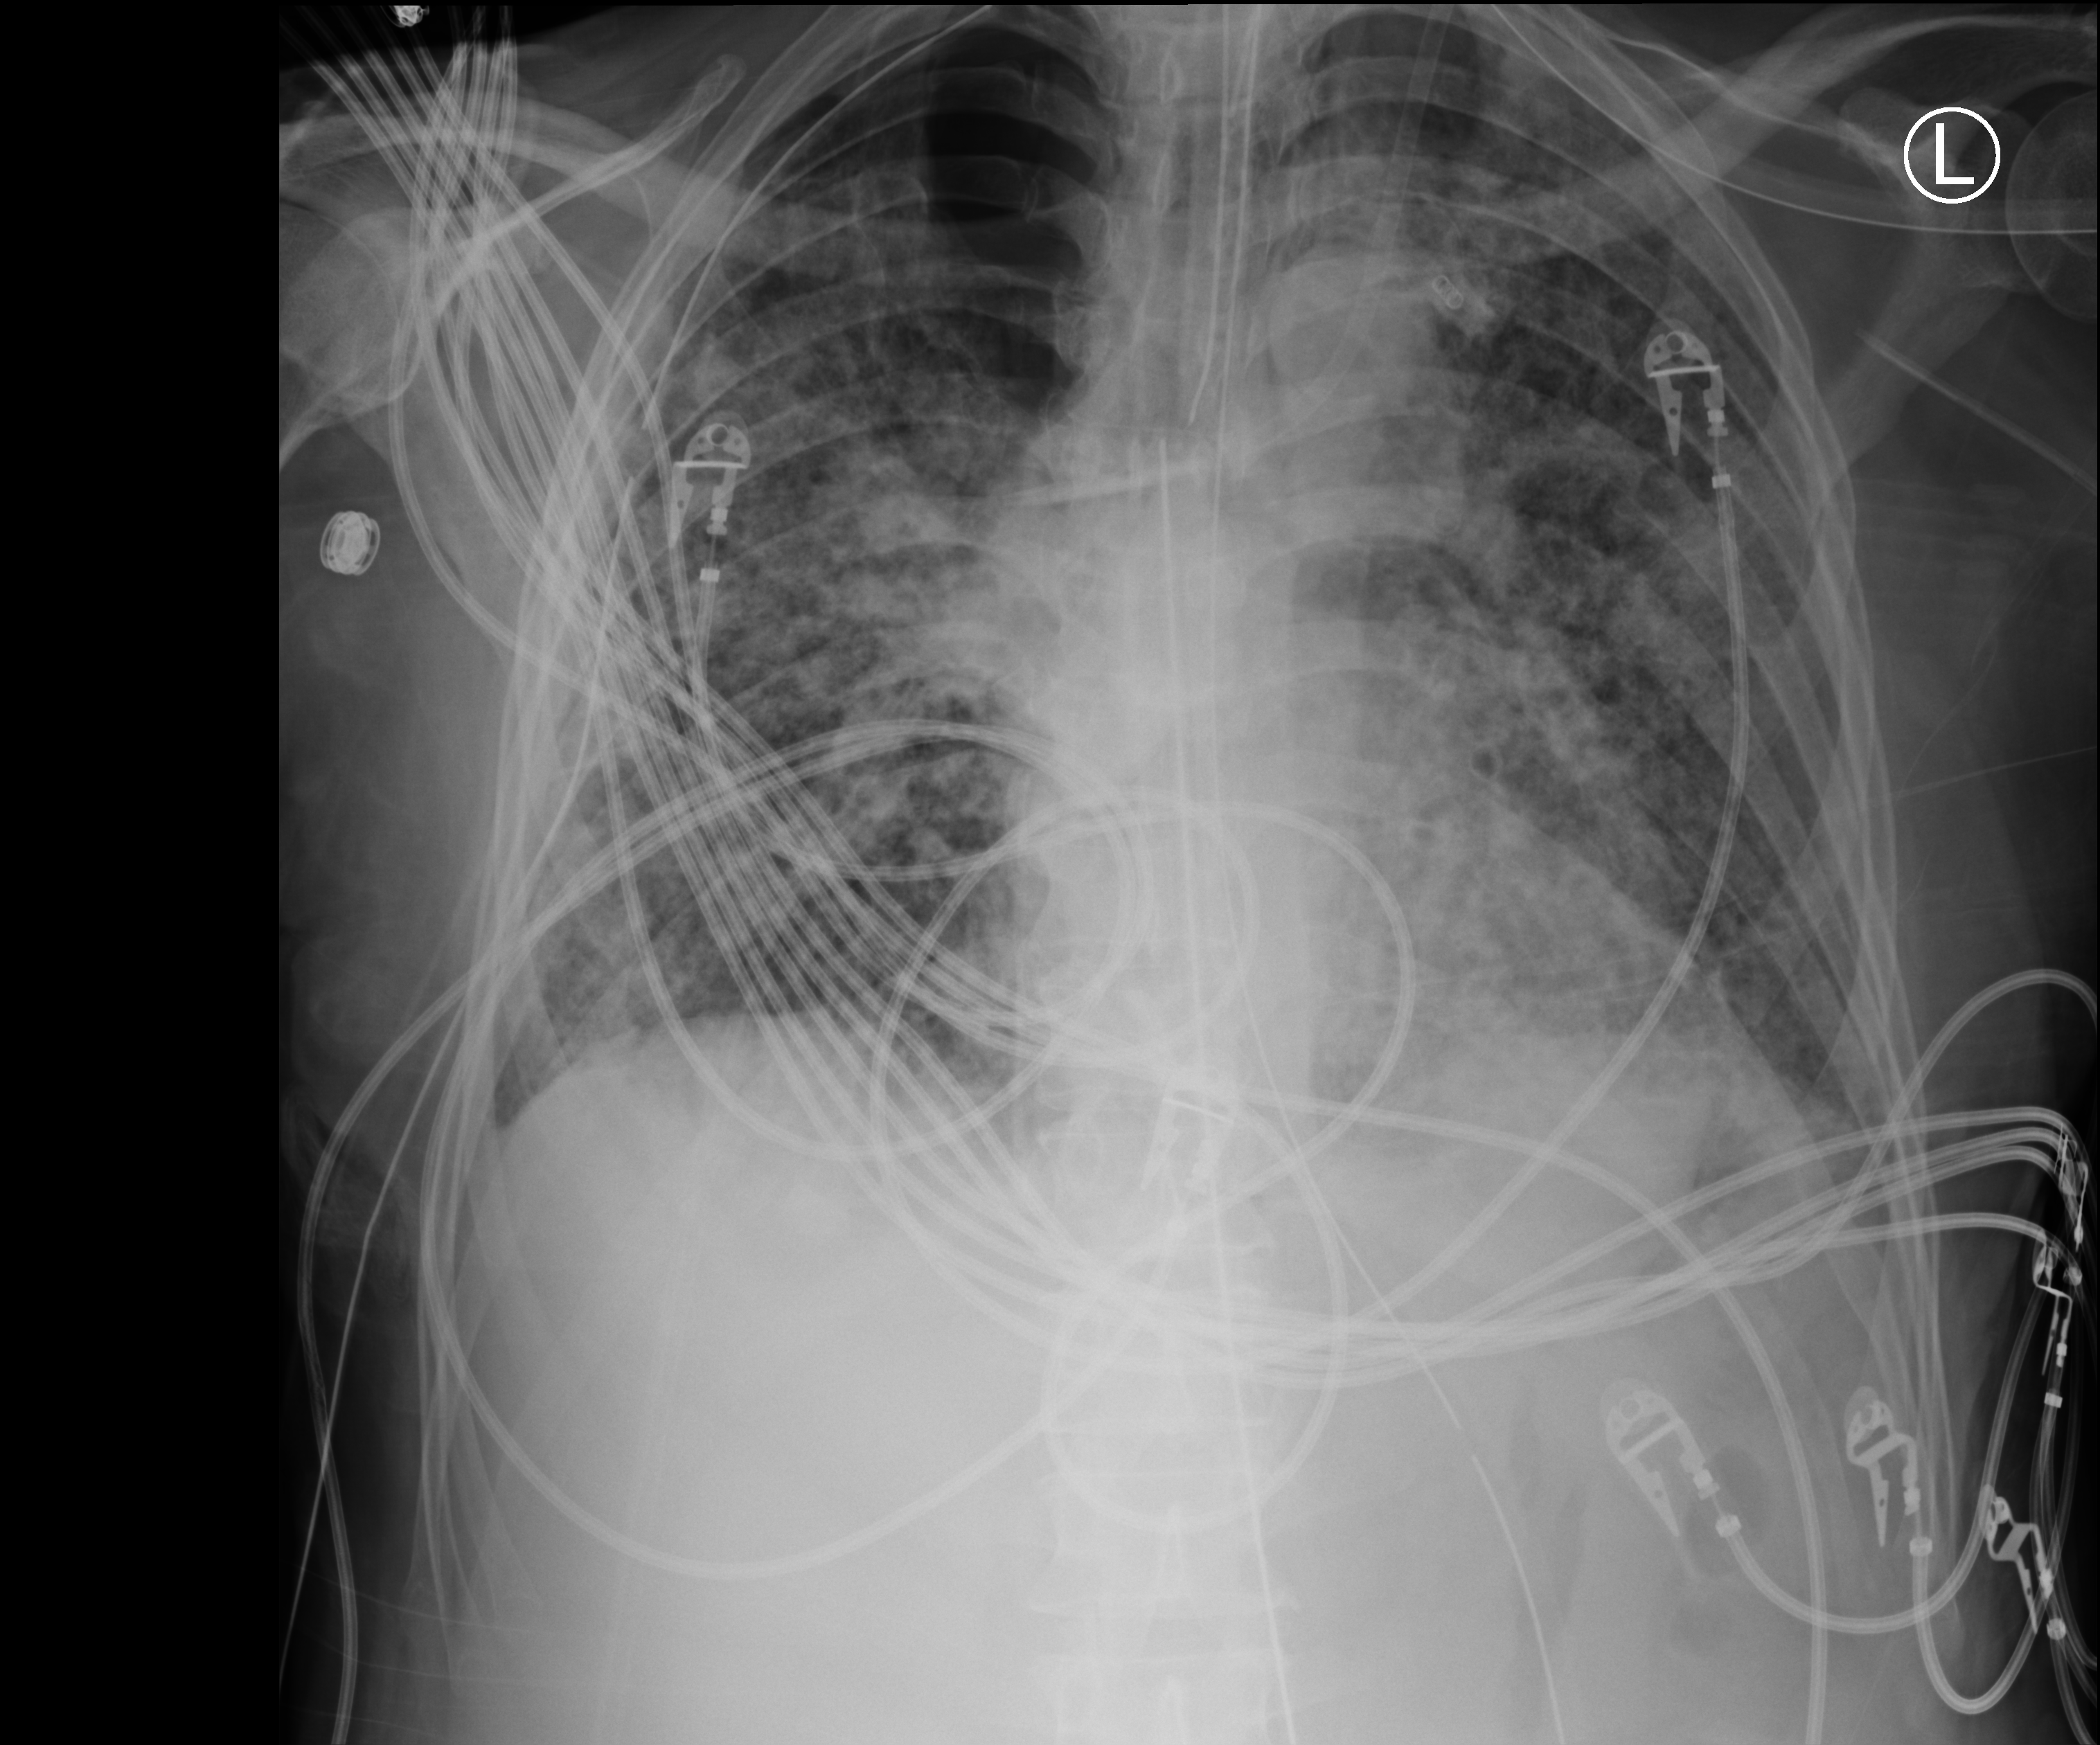
Chest X-ray (portable). Male patient hospitalised with COVID-19, age 60–74 years.
From the hospital-stay record, not from the radiograph (when in the stay this image was taken is not recorded):
- diabetes (admission record): no